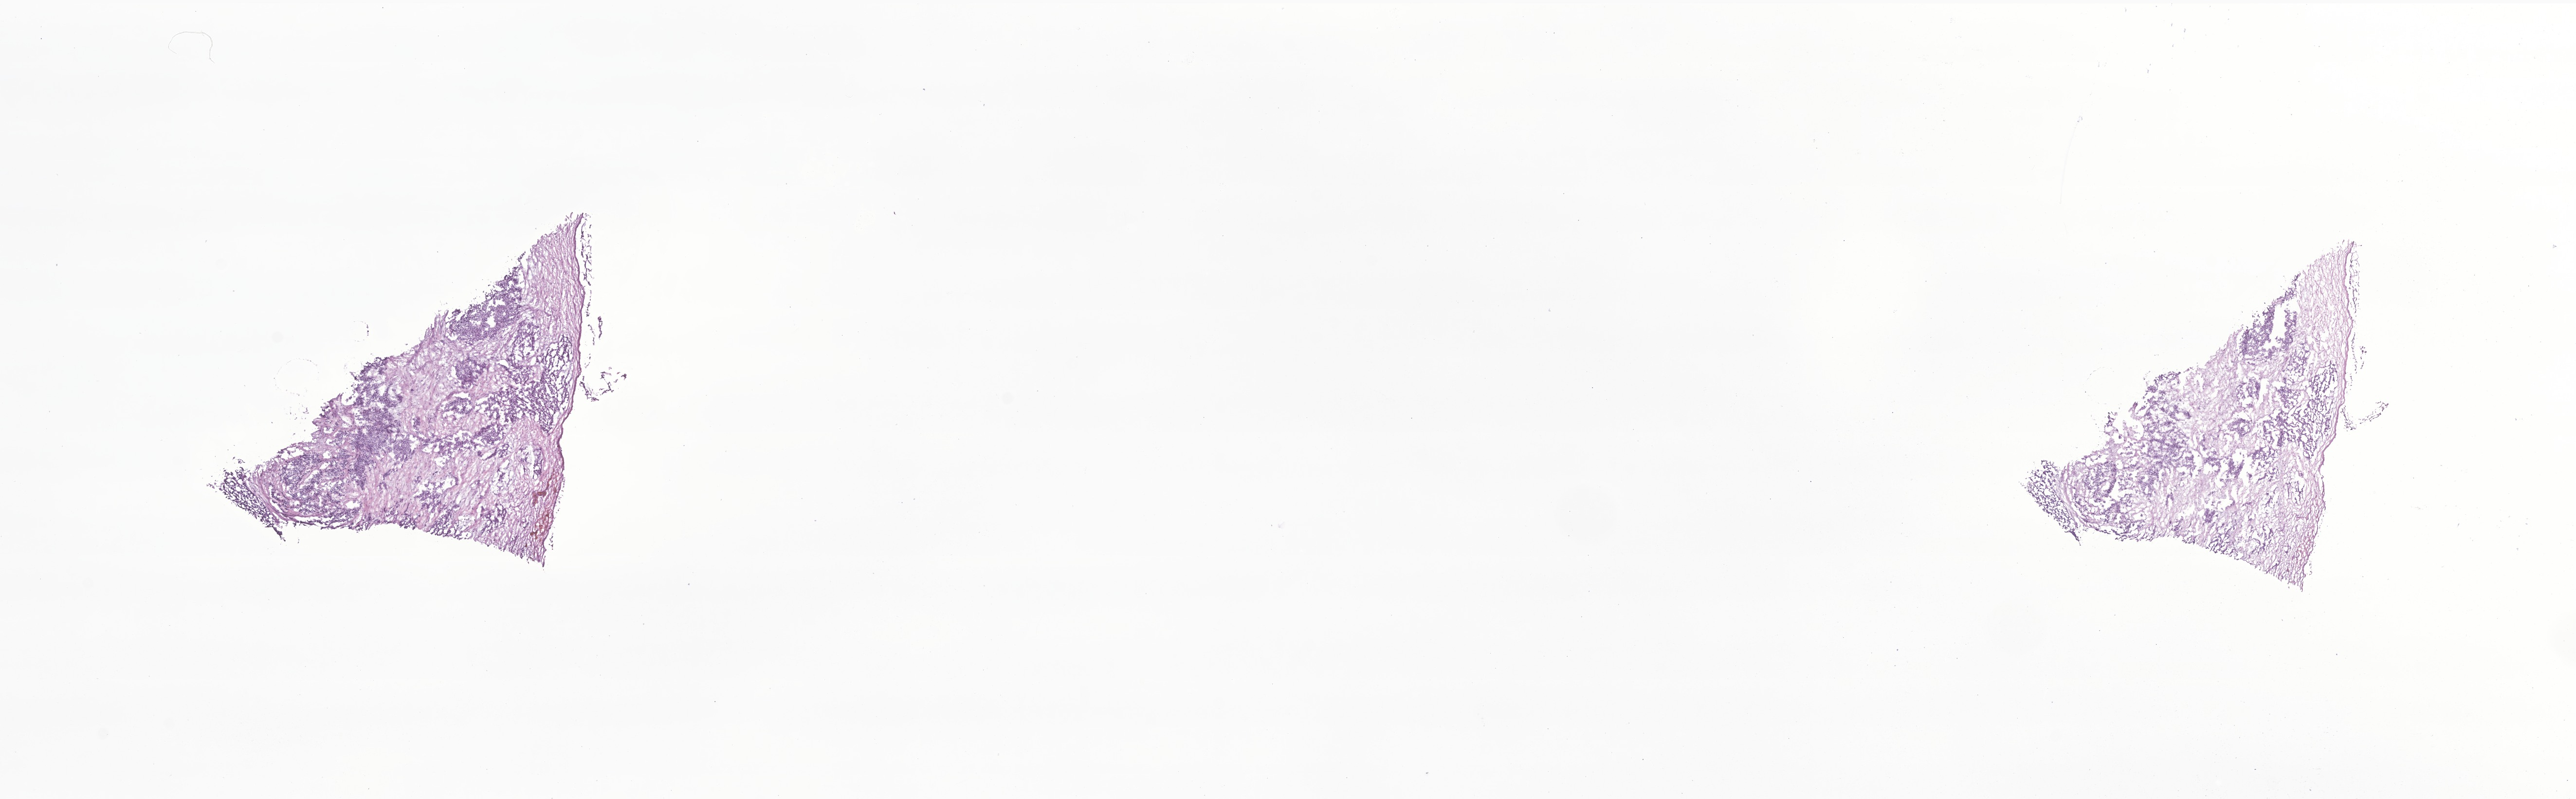
Whole-slide image, haematoxylin and eosin stain of tumor tissue from the soft tissue — a low-resolution overview of the entire scanned area, about 22.3 x 6.9 mm, frozen section (OCT-embedded). Patient: male, age 202 months.
• diagnosis: Desmoplastic small round cell tumor